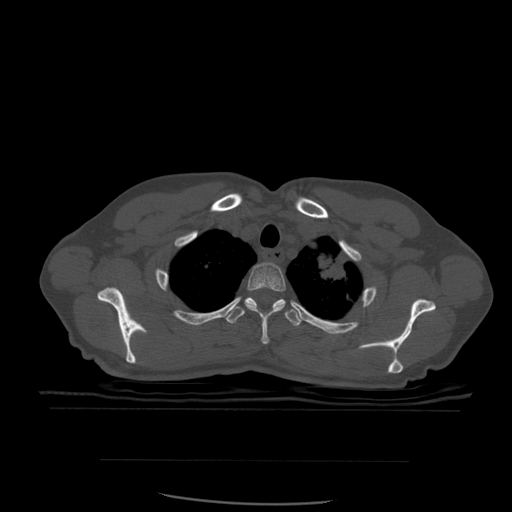
CT including the spine, one axial slice; bone window (W 1800 / L 400 HU); 1.25 mm slice thickness; 512 × 512 image matrix, field of view 392 × 392 mm. Patient age 48 years. Case-level facts recorded for this patient, not image findings: primary cancer: lung.
Structures marked on this image (semi-automatically segmented with operator editing):
- T2 vertebra: box from (x=245, y=263) to (x=286, y=345) px
- T3 vertebra: (x=226, y=297)–(x=302, y=327)